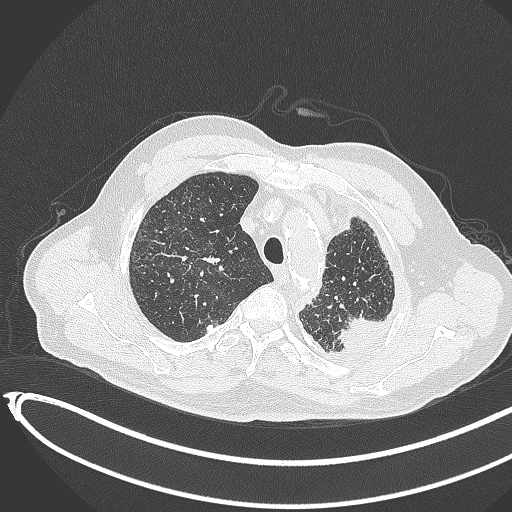
Chest CT, one axial slice. Position 348 of 451 along the scan axis. Reconstruction kernel B70f. Lung window (W 1500 / L -600 HU). 1 mm slice thickness. 512 × 512 image matrix, field of view 400 × 400 mm. Patient: male, 78 years. From the clinical record (not read from this slice): clinical TNM (as recorded): T1c N0 M1.
Structures marked on this image (rectangle marked by the reading radiologist):
- lung tumour (recorded histology: adenocarcinoma): bounding box [x1, y1, x2, y2] px = [335, 316, 384, 357]